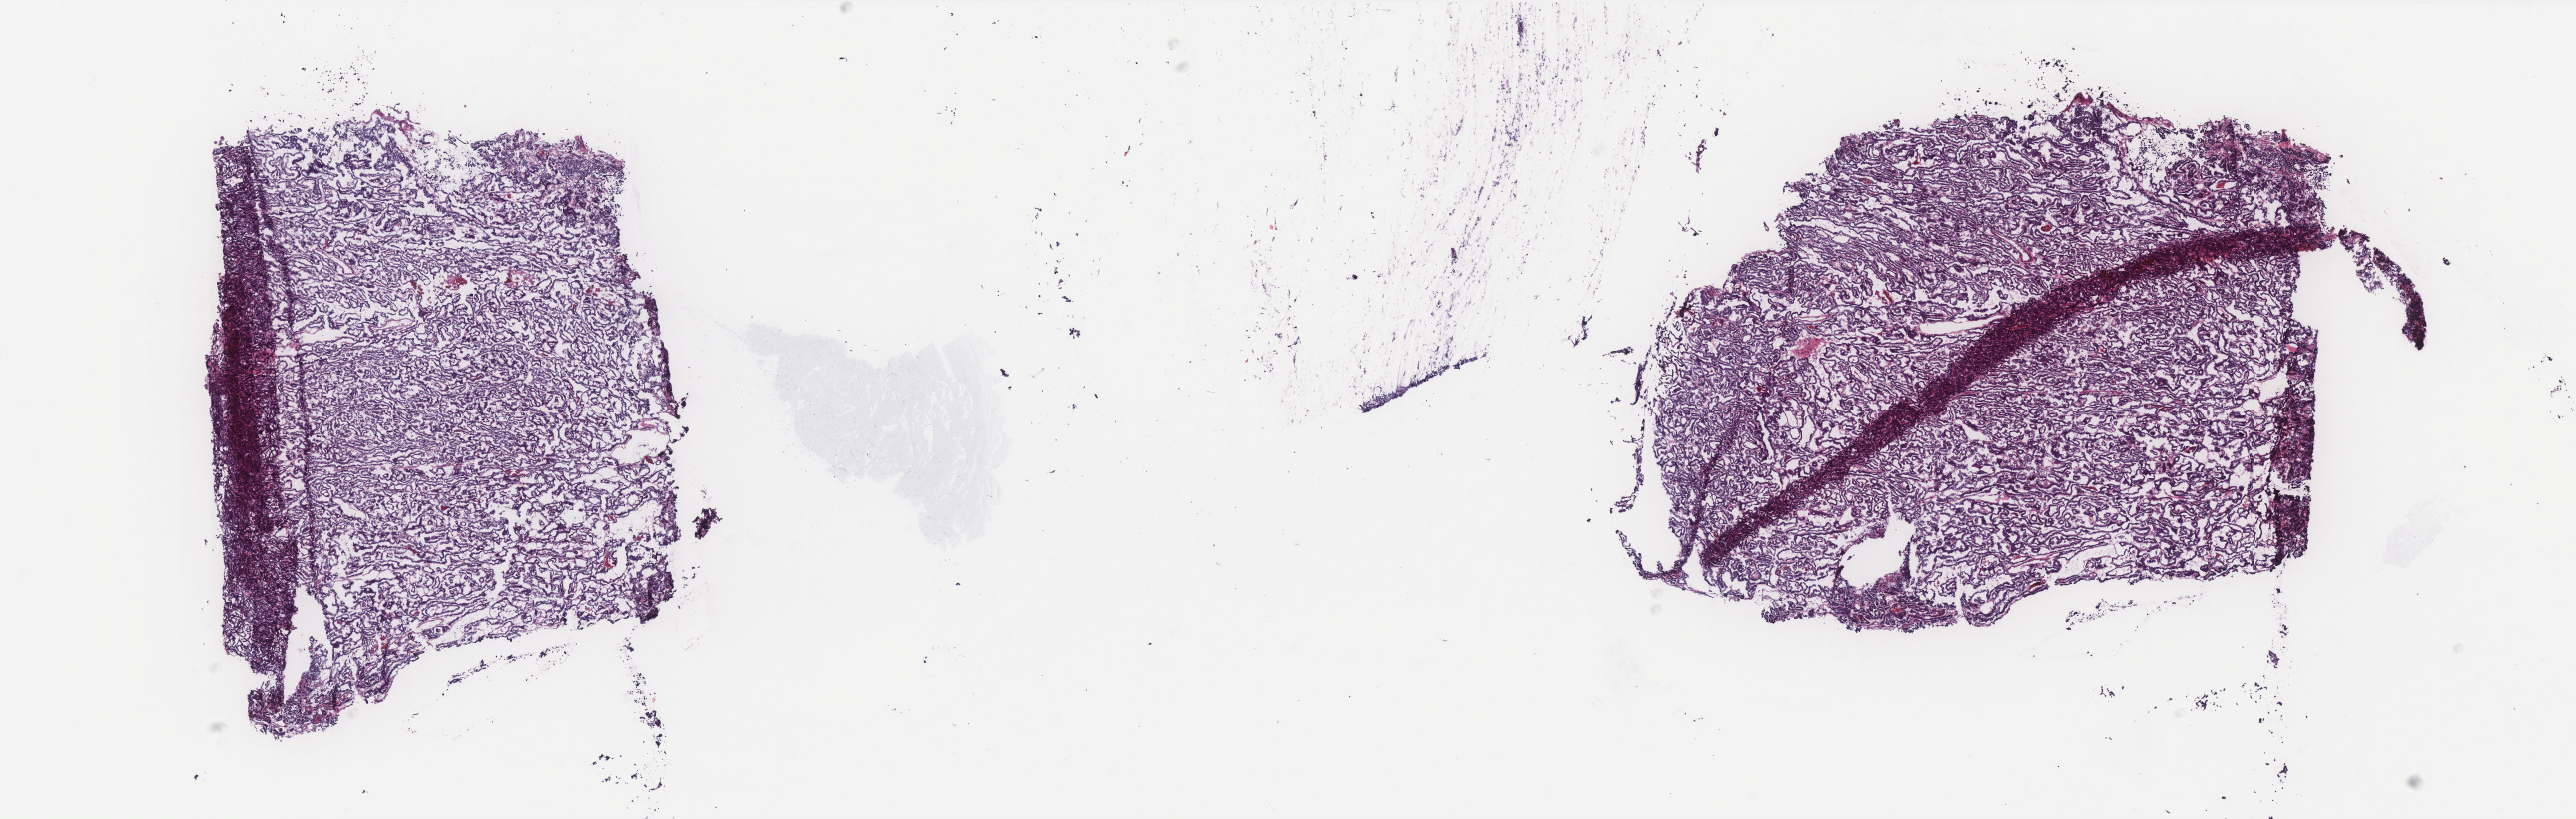
Digitized Hematoxylin and eosin (H&E) stained tissue section (whole slide) — a low-resolution overview of the entire scanned area, about 20.7 x 6.6 mm (from a 40x scan); frozen section from the bottom of the tissue portion; thyroid, primary tumour sample. Patient: male, age at initial diagnosis 58 years. Pathologist review of this section (percent, as recorded): tumour cells 85%, tumour nuclei 85%, normal cells 0%, stromal cells 15%, necrosis 0%. Inflammatory infiltration, as recorded: lymphocyte infiltration 1%, monocyte infiltration 0%, neutrophil infiltration 0%.
Diagnosis: Papillary adenocarcinoma, NOS (thyroid gland). AJCC pathologic stage: III (7th edition).